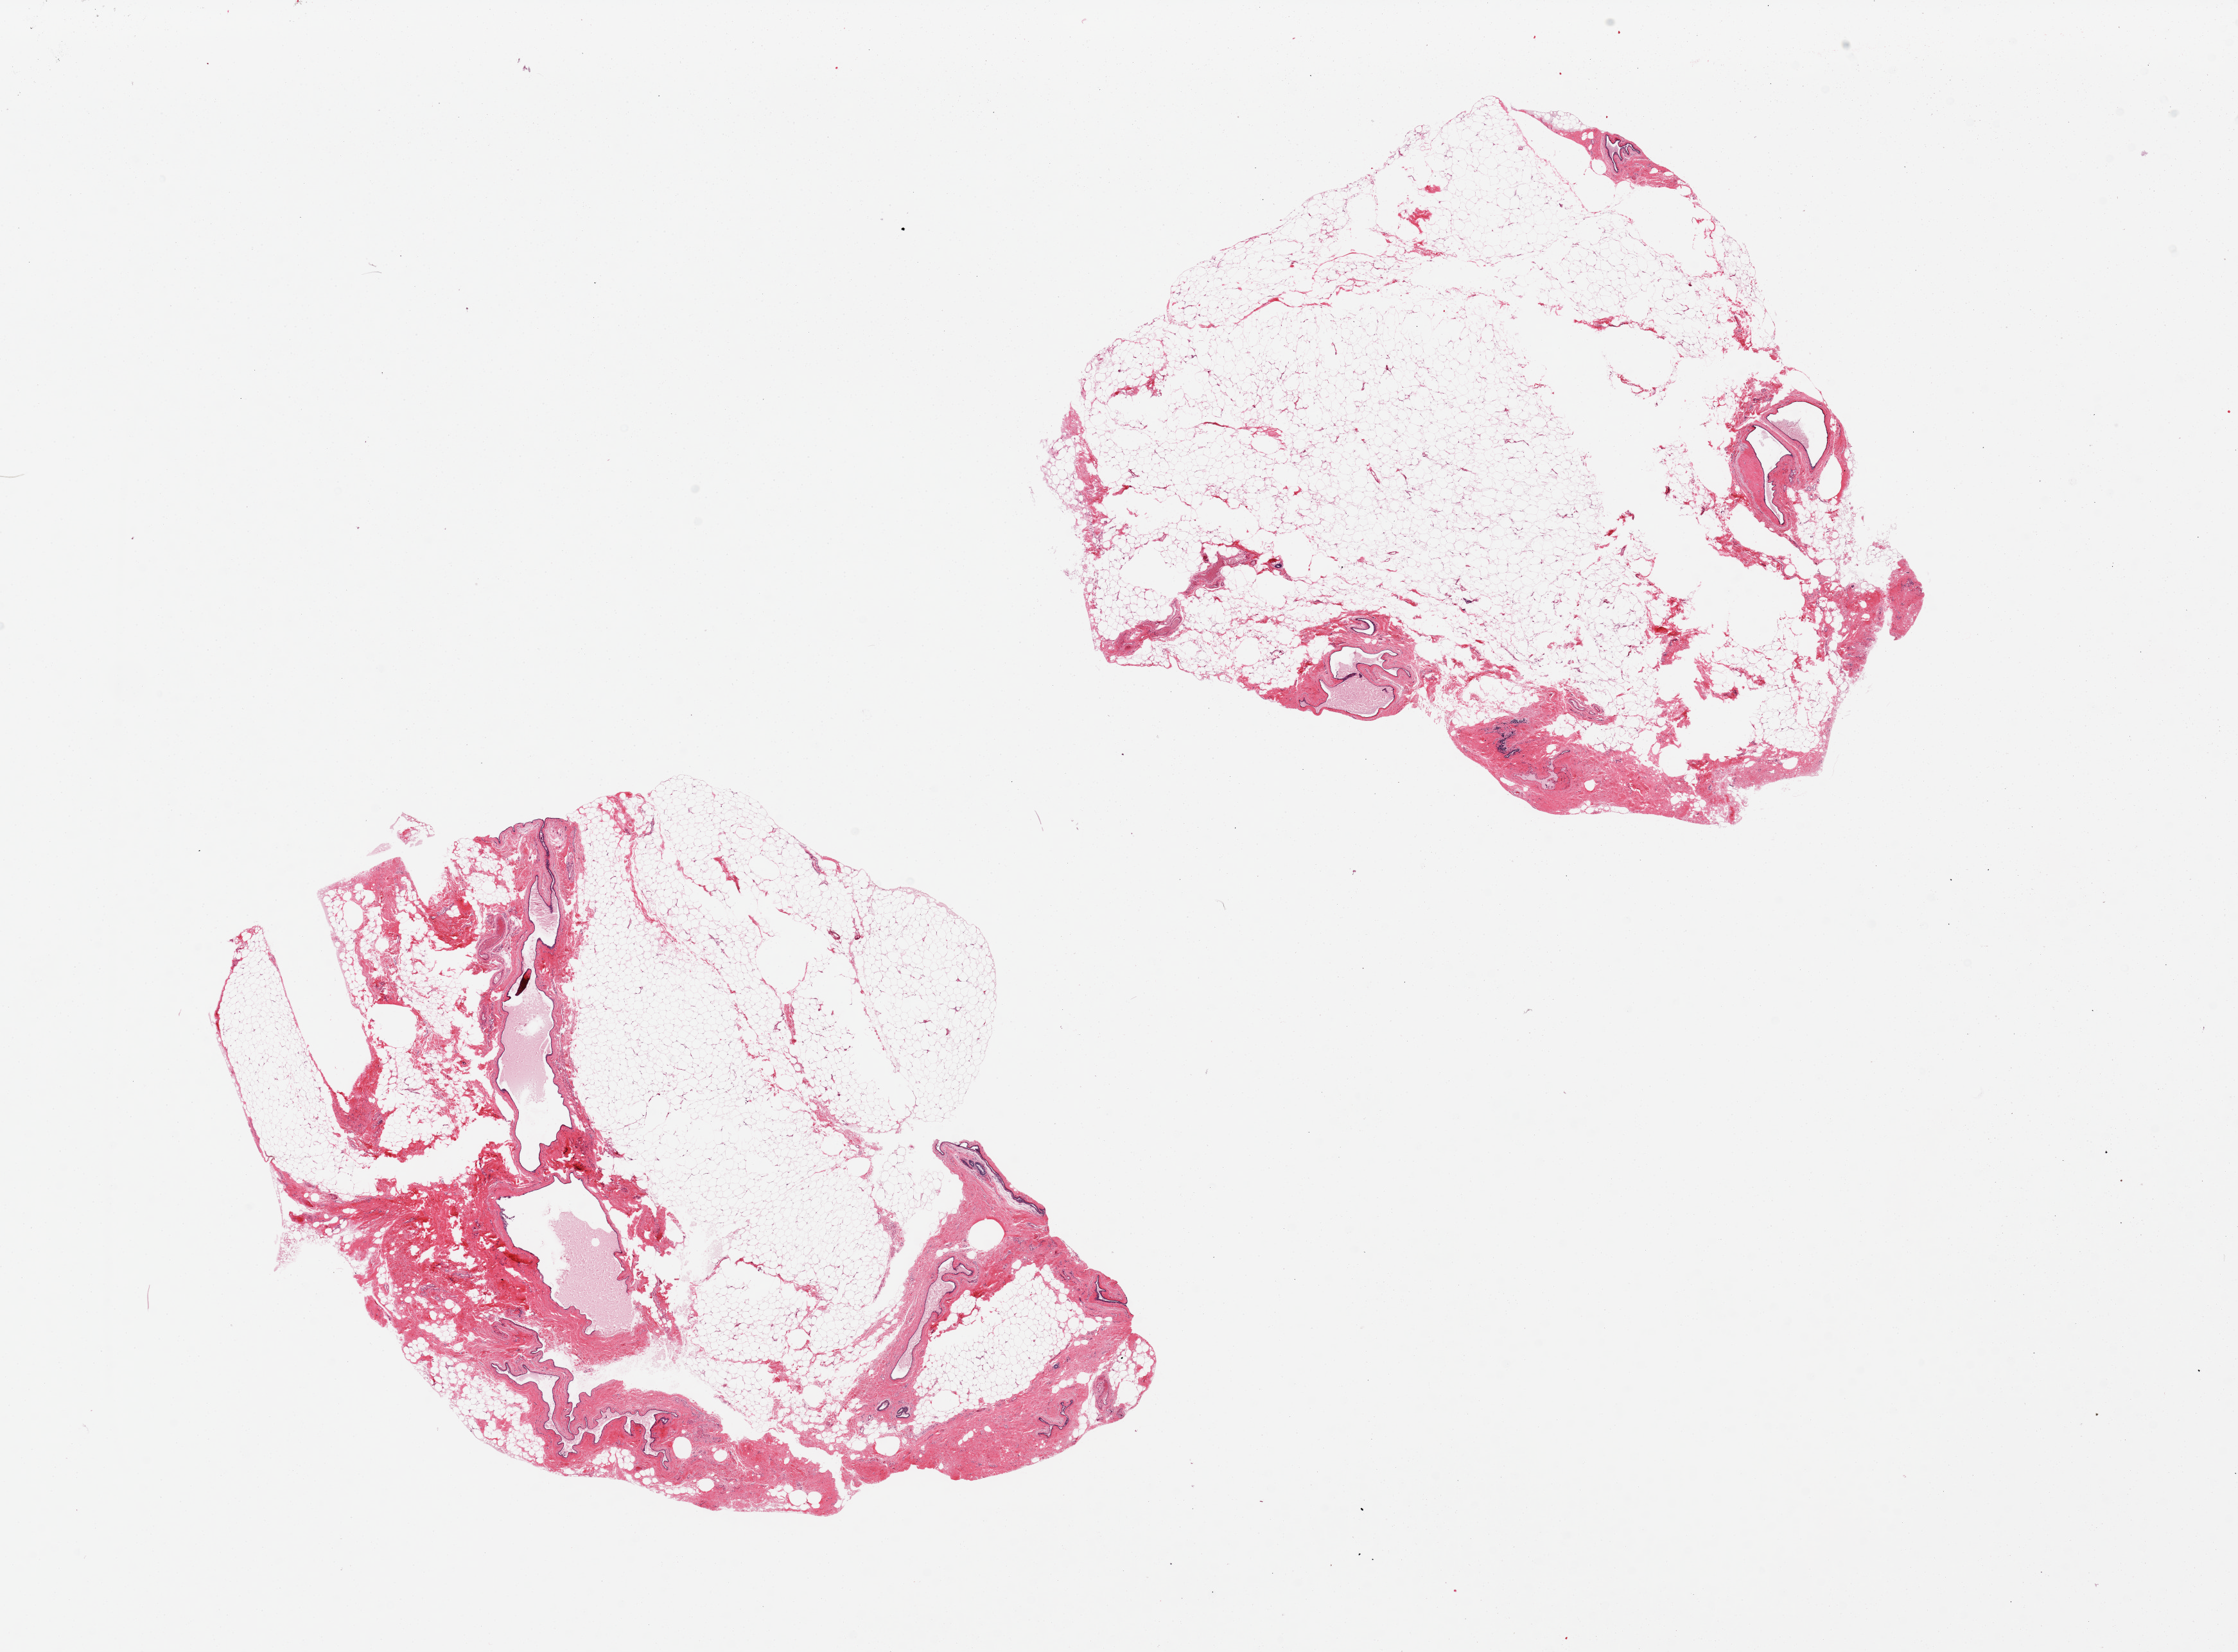
Haematoxylin and eosin whole-slide image, brightfield — whole scanned area (about 27.6 x 20.4 mm) shown as a low-resolution overview. PAXgene-fixed, paraffin-embedded tissue. Sampled site (target tissue): breast. Tissue donor sample. Female donor.
Review note (as recorded): 2 pieces, ~40% fibrous tissue.